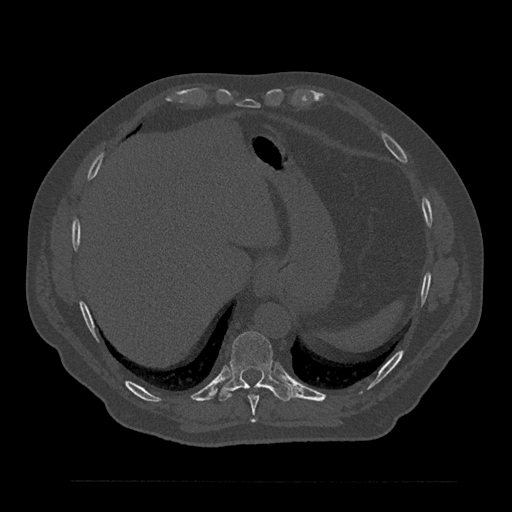
CT including the spine, one axial slice; position 369 of 797 along the scan axis; reconstruction kernel Br40s/3; 120 kVp; bone window (W 1800 / L 400 HU); 512 × 512 image matrix, field of view 430 × 430 mm. Male patient, age 61 years. From the clinical record (not read from this slice): primary cancer: prostate.
Annotated regions visible in this slice (semi-automatically segmented with operator editing):
- T10 vertebra: box from (x=220, y=331) to (x=293, y=402) px
- T9 vertebra: (x=248, y=386)–(x=263, y=422)